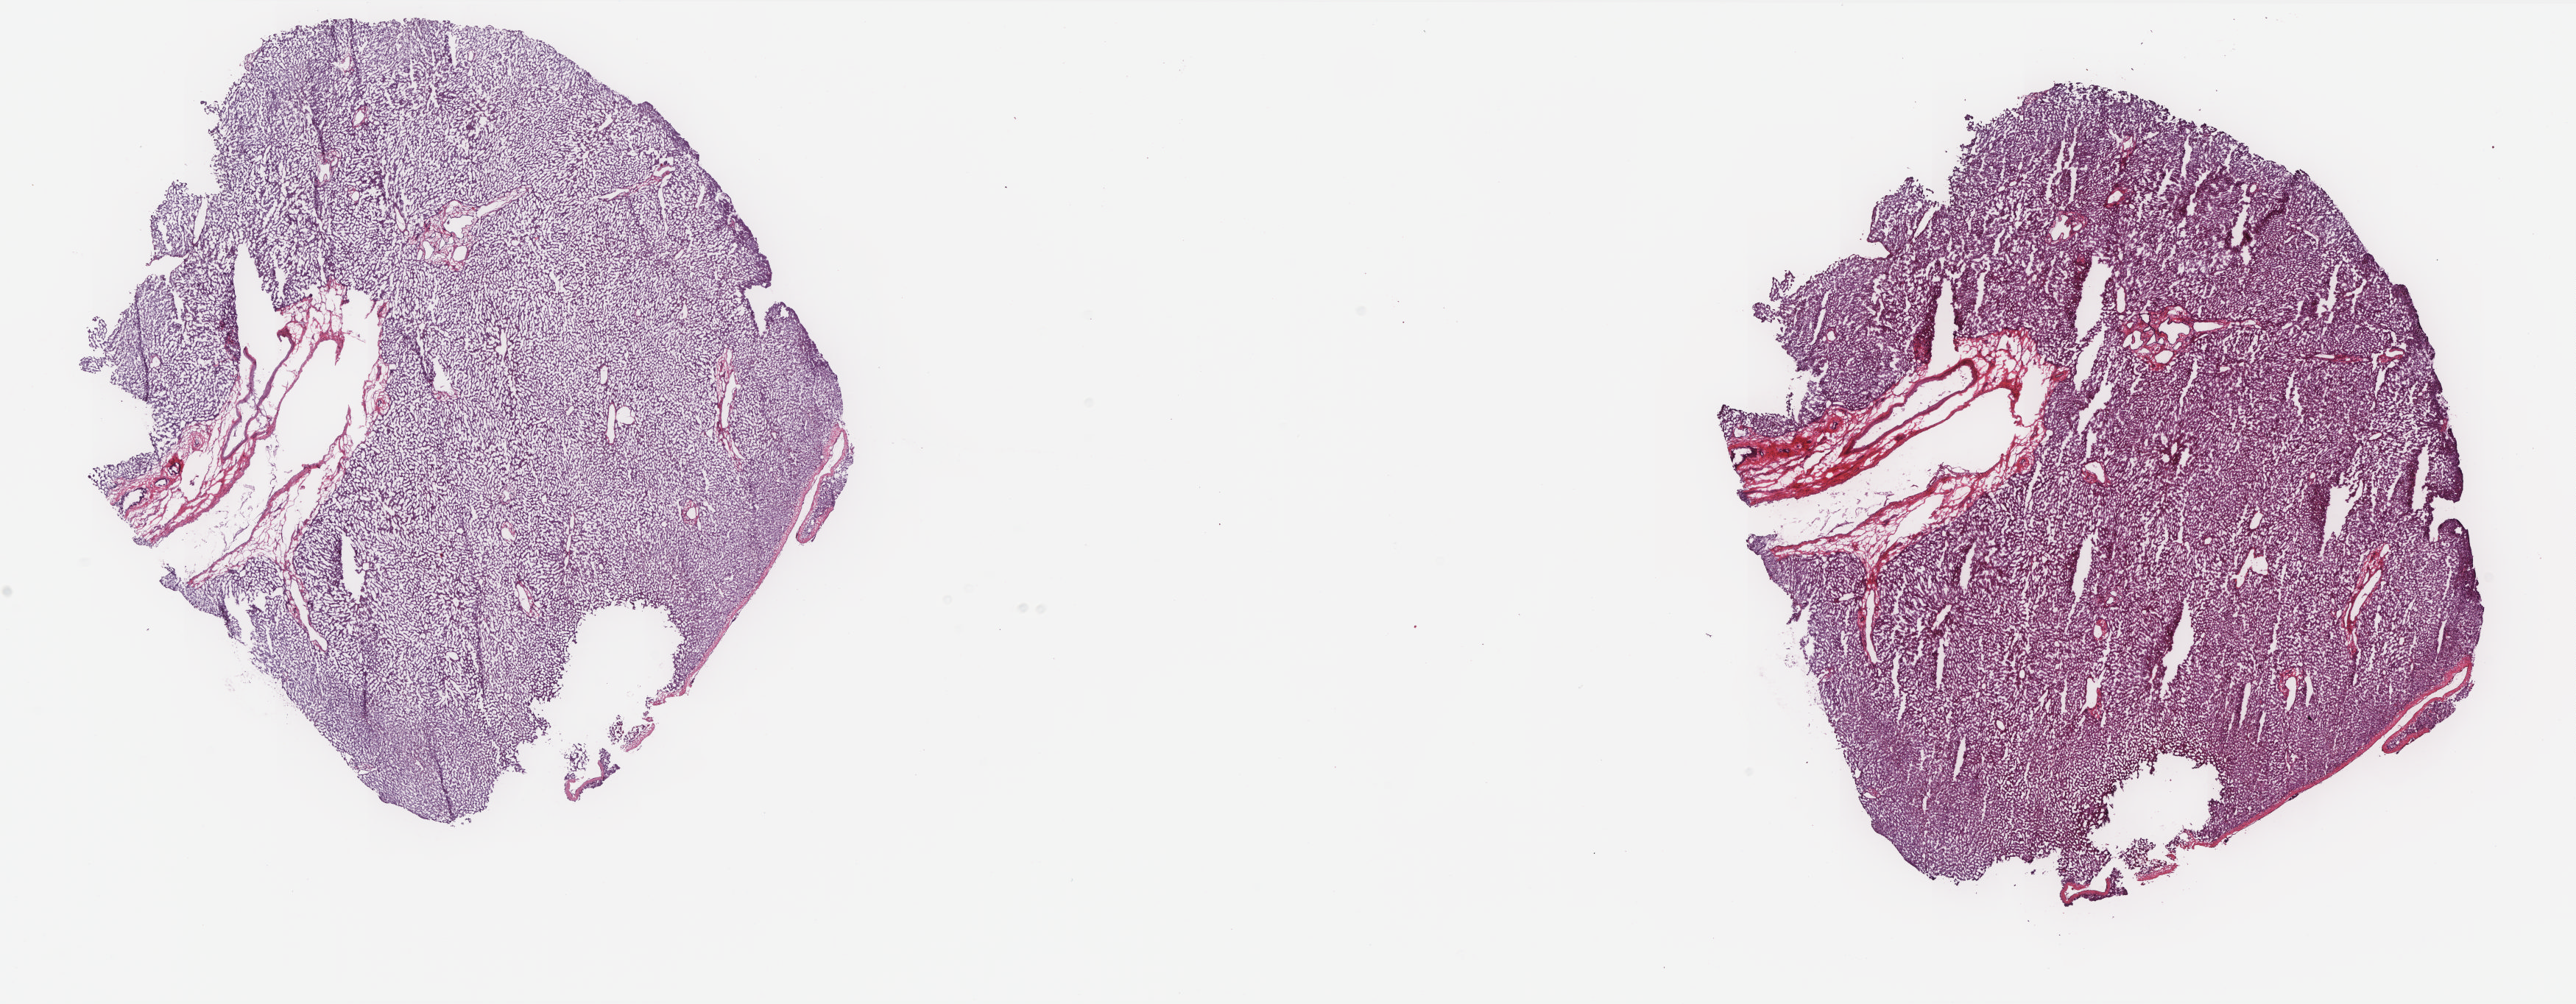
H&E whole-slide image, shown as a low-resolution overview of the whole scanned area (about 27.9 x 10.9 mm, slide scanned at 20x), frozen section from the top of the tissue portion, liver, solid tissue normal (non-tumour tissue) sample. Female patient; age at initial diagnosis 66 years. Pathologist review of this section (percent, as recorded): tumour cells 0%, tumour nuclei 0%, normal cells 100%, stromal cells 0%, necrosis 0%. Infiltration values recorded for this section: lymphocyte infiltration 0%, monocyte infiltration 0%, neutrophil infiltration 0%.
This section: solid tissue normal sample (biorepository sample class). Patient diagnosis: Hepatocellular carcinoma, NOS.